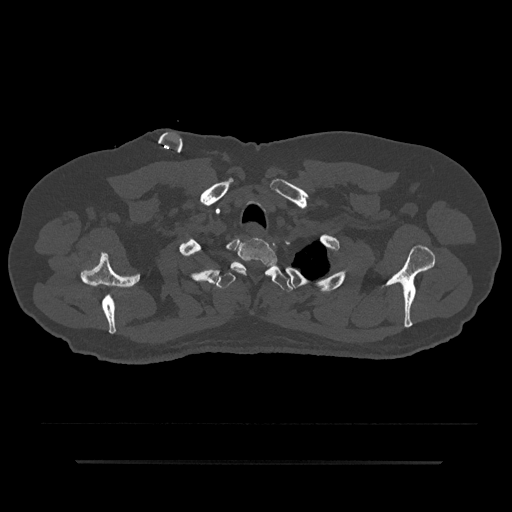
CT including the spine, one axial slice; slice 718 of 797 in the series (ordered by position); 120 kVp; bone window (W 1800 / L 400 HU); 512 × 512 image matrix. Patient: male, 59 years. From the clinical record (not read from this slice): primary cancer: bile ducts.
Annotated regions visible in this slice (semi-automatic segmentation, software-assisted and operator-edited):
- T1 vertebra: bounding box <231,238,278,276> (left, top, right, bottom; pixels)
- T2 vertebra: <215,263,293,292>